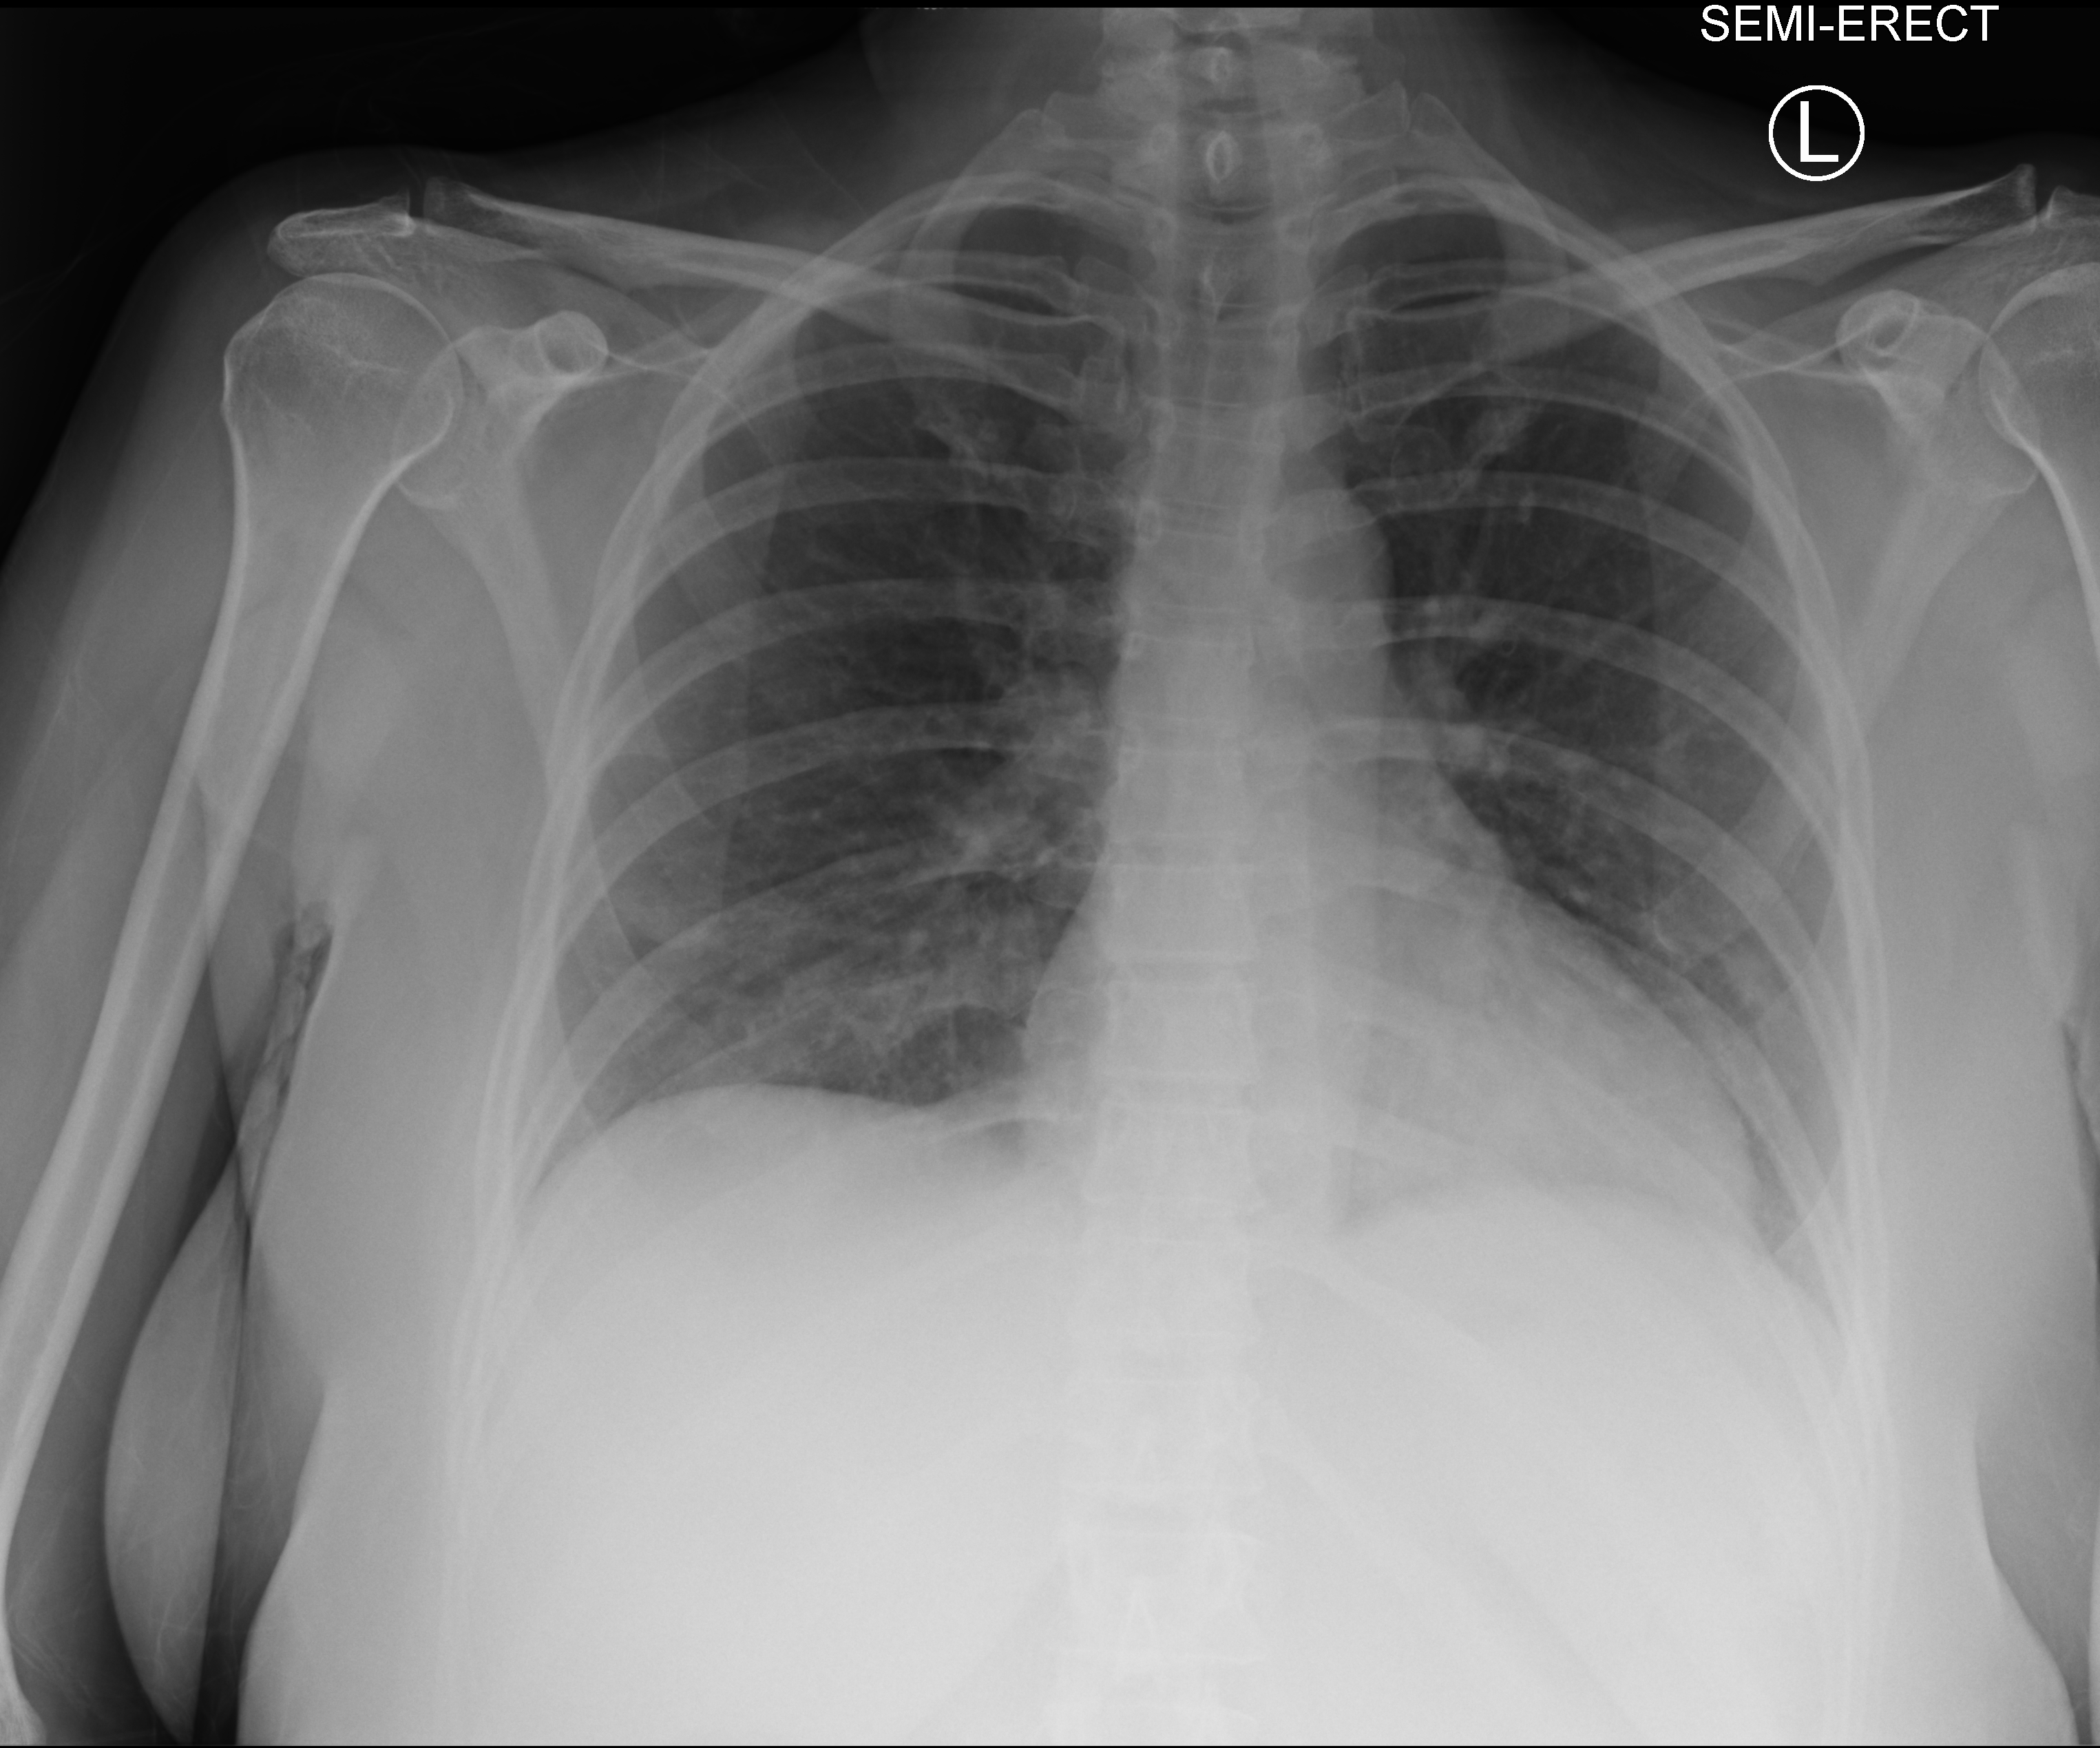
Bedside chest radiograph (computed radiography), anteroposterior (AP) projection. Female patient hospitalised with COVID-19, age 18–59 years.
Admission-level facts for this patient (not findings on this image; timing relative to this image not recorded): mechanically ventilated during this hospital stay: no.